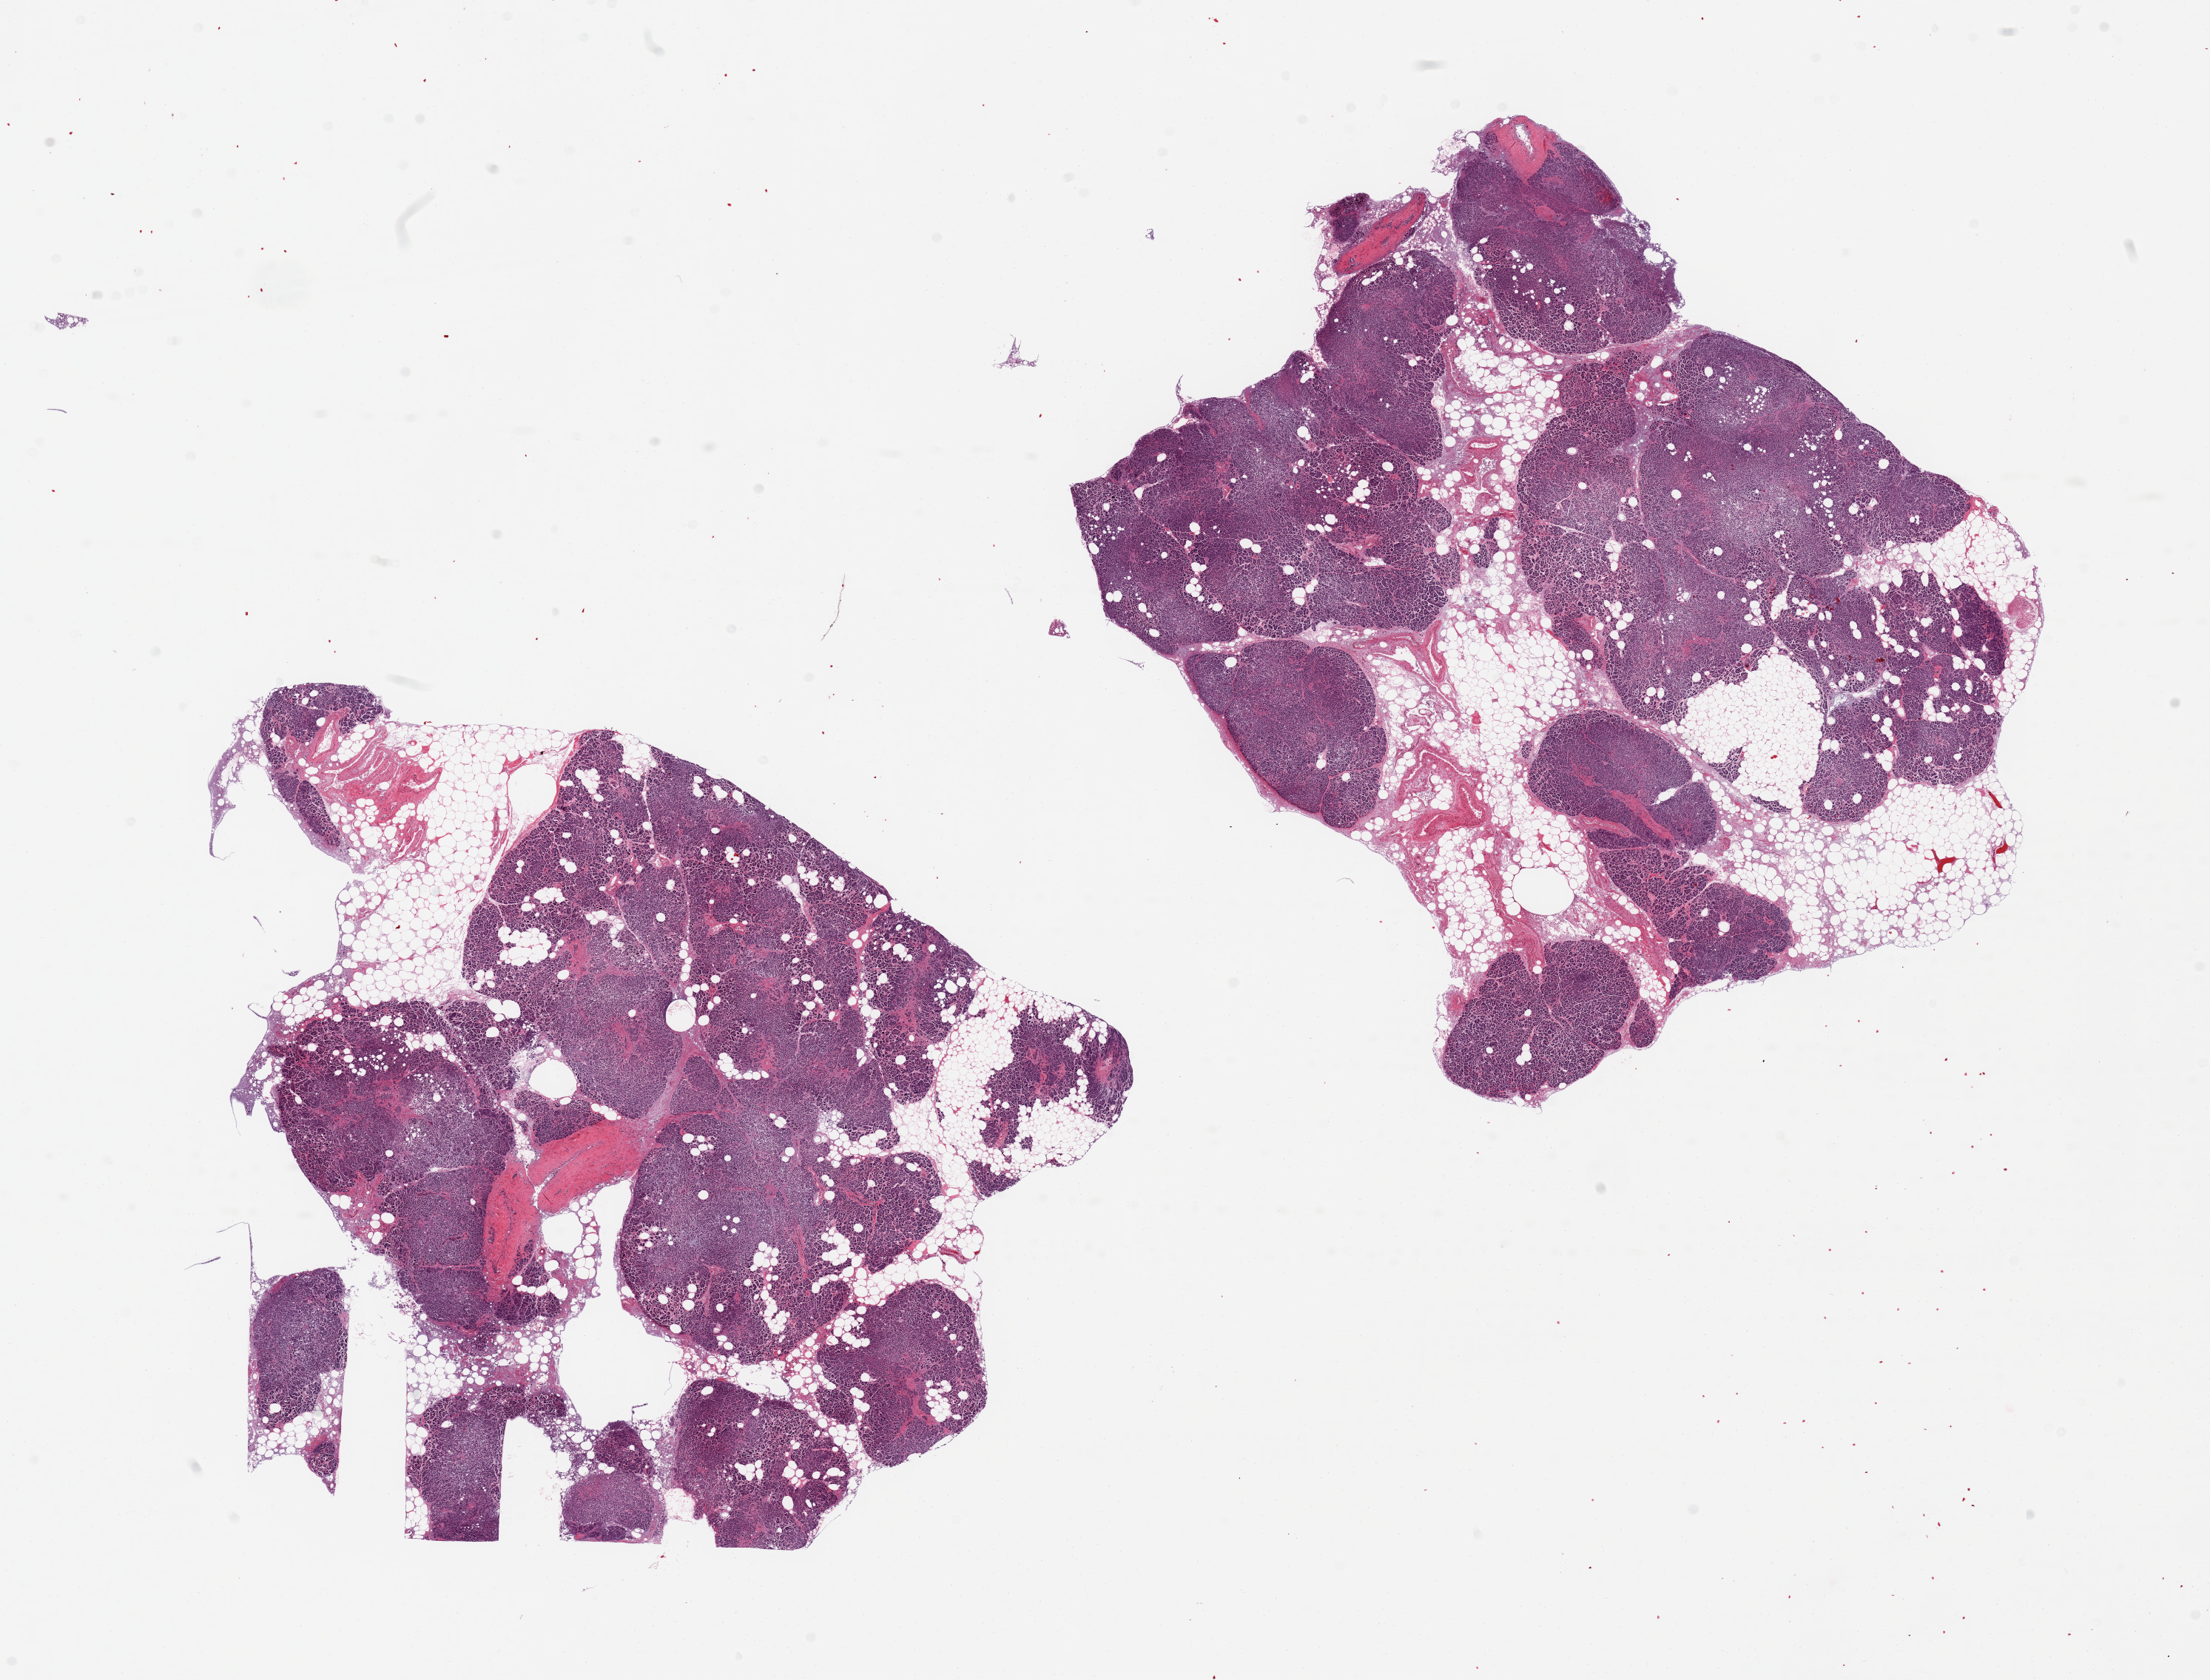
H&E whole-slide image, whole scanned area (about 23.6 x 18.0 mm, from a 20x scan) shown as a low-resolution overview; PAXgene-fixed, paraffin-embedded tissue; sampled site (target tissue): pancreas; donor tissue sample.
Review note (as recorded): 2 pieces, marked autolysis/saponification, Islets not well visualized; interstitial fat is ~30%.